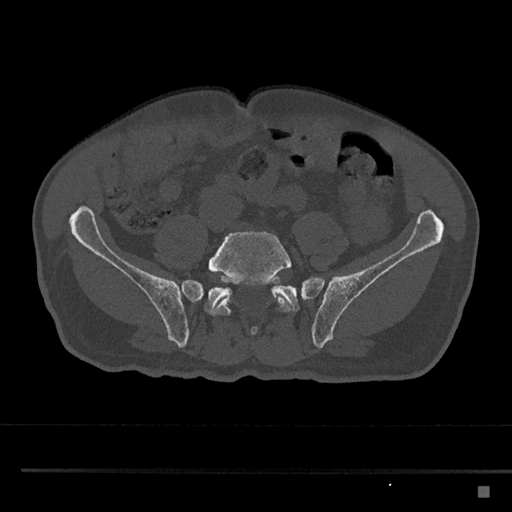
CT including the spine, one axial slice. Slice 565 of 797 in the series (ordered by position). Reconstruction kernel Br40s/3. 120 kVp. Bone window (W 1800 / L 400 HU). 0.5 mm slice thickness. 512 × 512 image matrix, field of view 391 × 391 mm. Male patient, age 59 years. Case-level facts recorded for this patient, not image findings: primary cancer: prostate.
Annotated regions visible in this slice (semi-automatically segmented with operator editing):
- L5 vertebra: box from (x=208, y=231) to (x=291, y=335) px